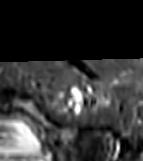
MRI of an extremity soft-tissue mass, one axial slice. Slice 62 of 81 in the series (ordered by position). STIR. MR volume resampled by the dataset authors to the PET/CT grid (not the native acquisition matrix). 3.27 mm slice thickness. 143 × 161 image matrix, field of view 140 × 157 mm. Female patient. Case-level facts recorded for this patient, not image findings: histological type: myxofibrosarcoma; grade: intermediate; site of the primary tumour: left thigh.
Outlined on this slice (expert contour drawn on MRI and transferred to this co-registered scan by the dataset authors):
- gross tumour volume including surrounding oedema: bounding box <67,88,86,107> (left, top, right, bottom; pixels)